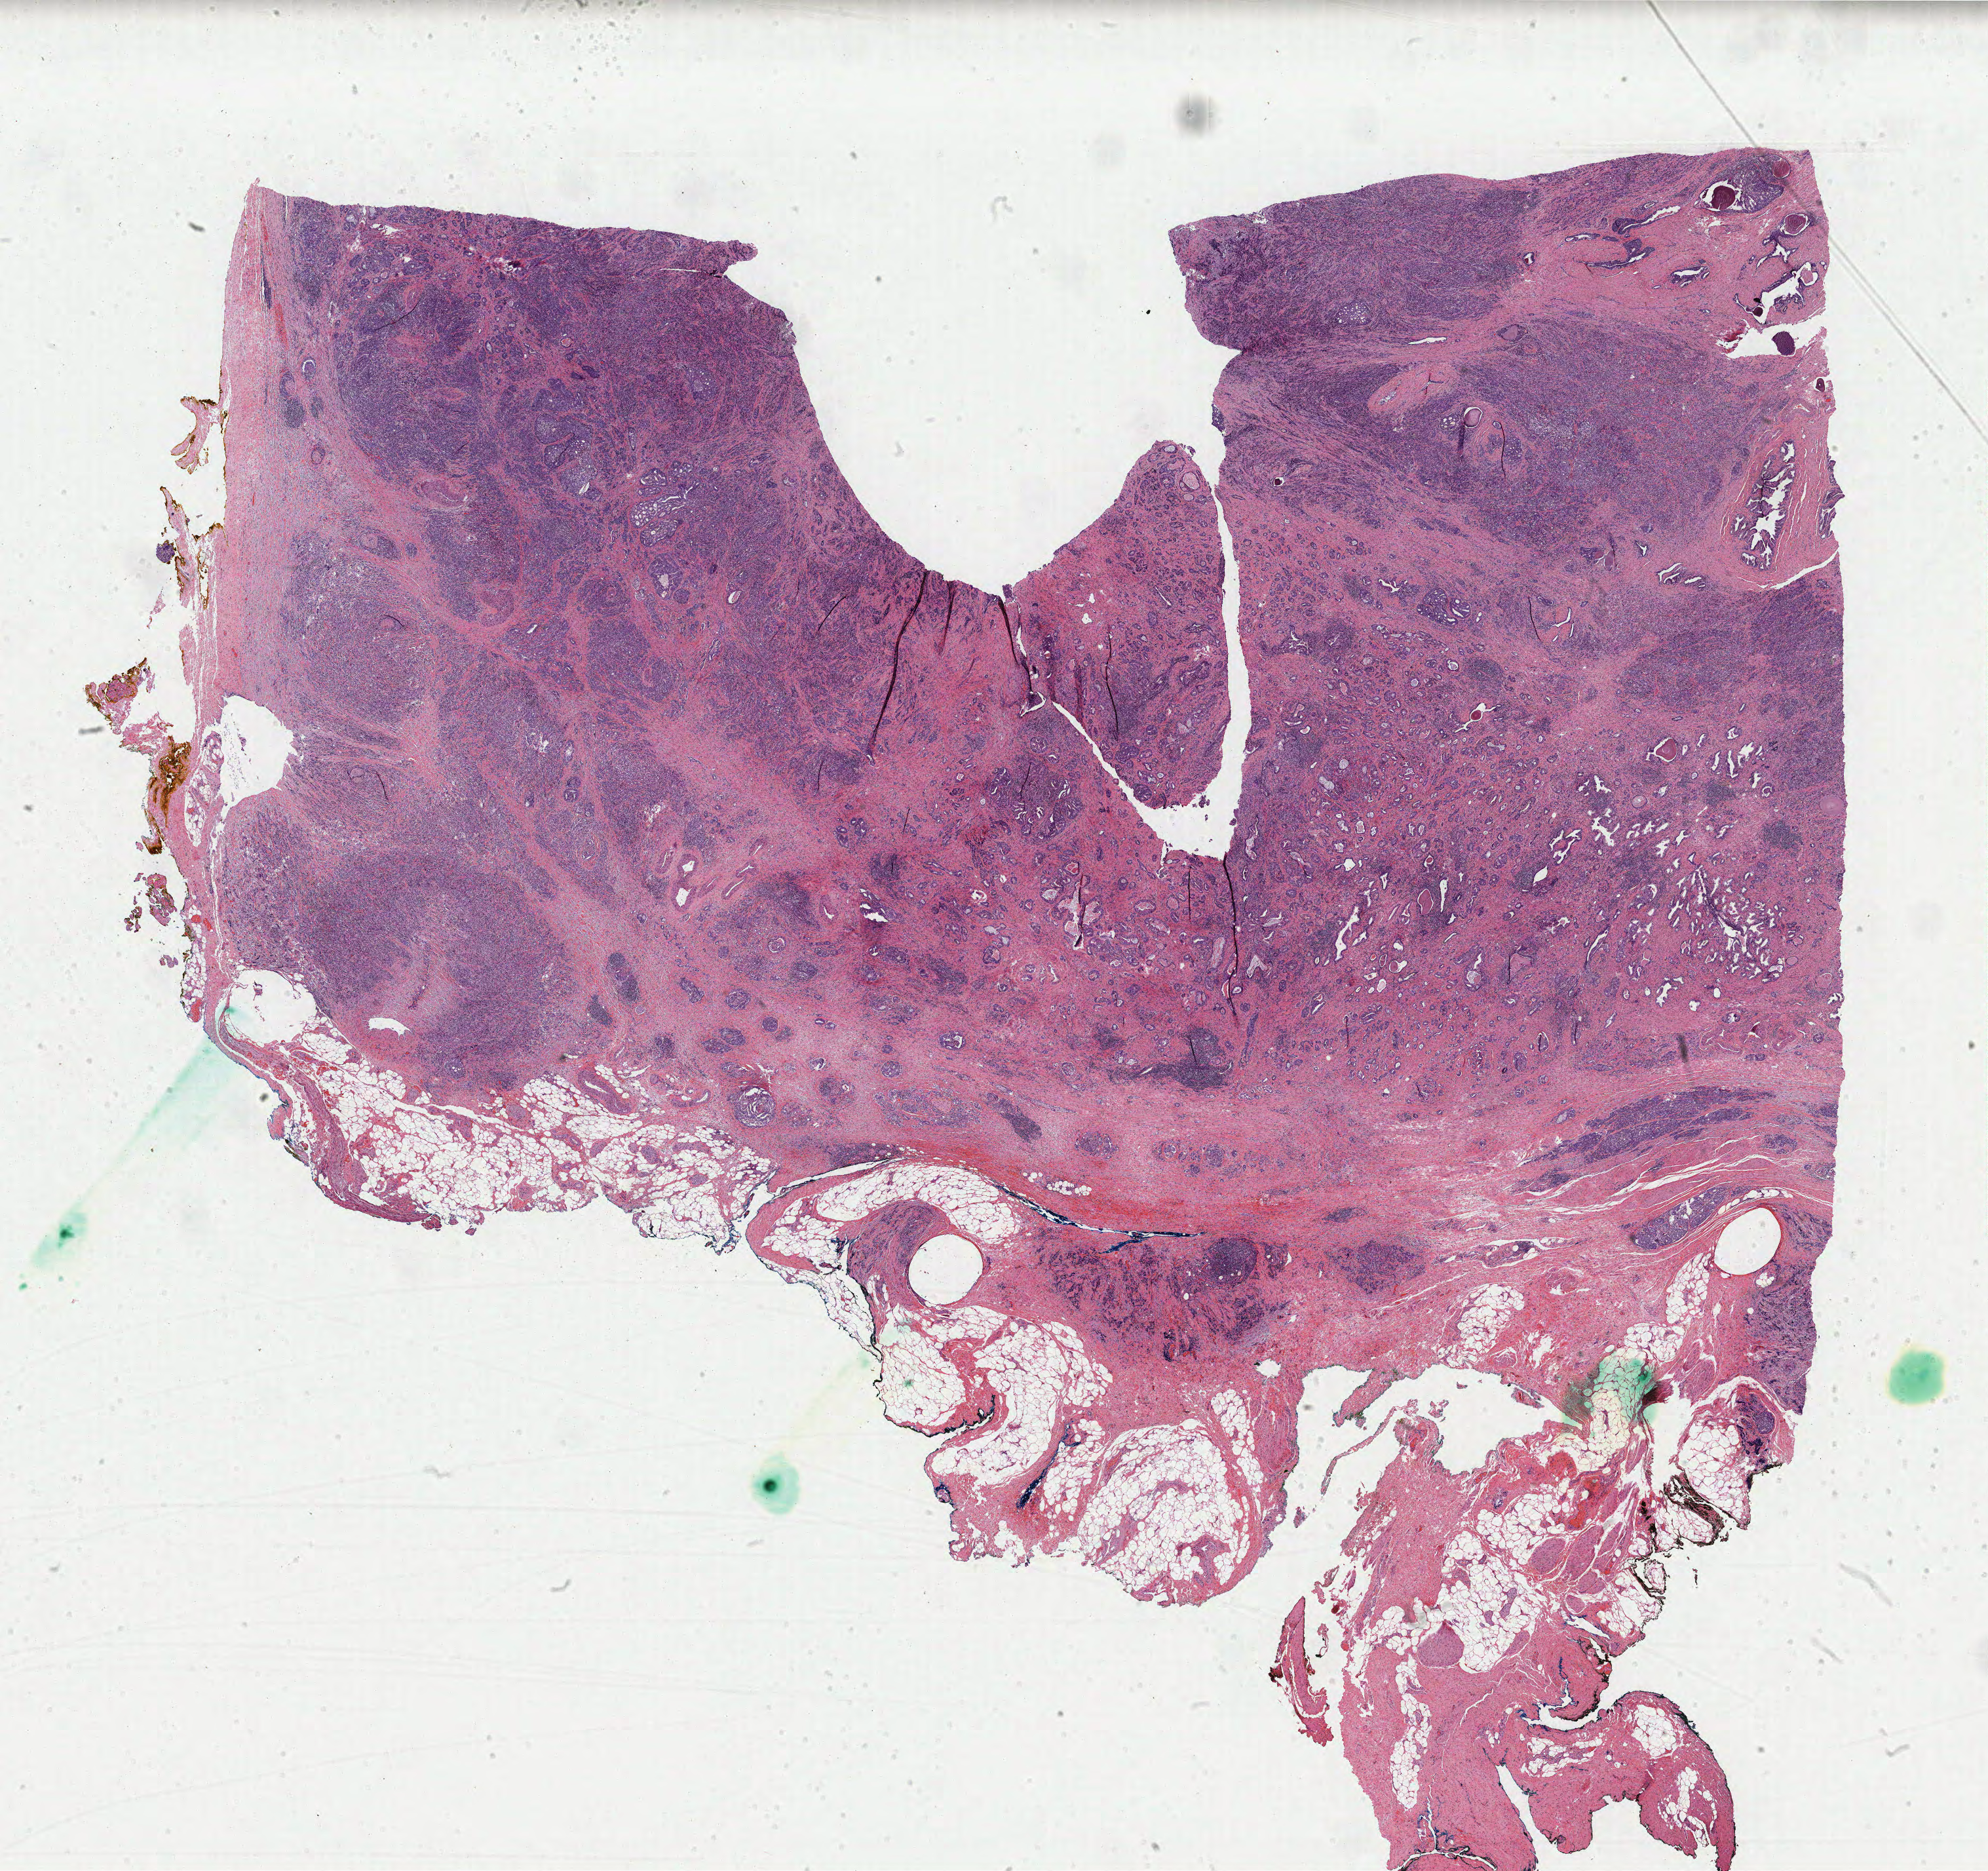
Digitized H&E tissue section (whole slide), whole scanned area (about 24.1 x 22.7 mm, acquisition: 40x scan) shown as a low-resolution overview. FFPE section. Primary tumour sample from the prostate. Patient: male, age at initial diagnosis 64 years. Gleason score: 9 (4+5).
* lymph nodes positive (case pathology): 8 of 20 examined
* histologic diagnosis: Adenocarcinoma, NOS (prostate gland)